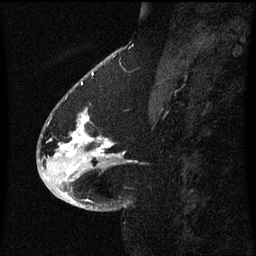
Breast MRI (dynamic contrast-enhanced), one sagittal slice. Position 24 of 60 along the scan axis. Dynamic contrast-enhanced series, image 2 of 3 at this slice position (ordered by acquisition). 1.5 T. TE 4.2 ms, TR 8.4 ms. 2 mm slice thickness. 256 × 256 image matrix. Female patient, age 54 years. From the clinical record (not read from this slice): setting: breast cancer imaged before/during neoadjuvant chemotherapy; receptor status: HR-positive, HER2-negative.
Annotated regions visible in this slice (semi-automatic segmentation, software-assisted and operator-edited):
- analysis volume of interest (the breast-tissue region the enhancement analysis was run in; not a lesion): box from (x=46, y=106) to (x=123, y=171) px
- tumour enhancement mask (voxels above the 70 % enhancement threshold inside the analysis volume of interest): (x=67, y=116)–(x=113, y=157)